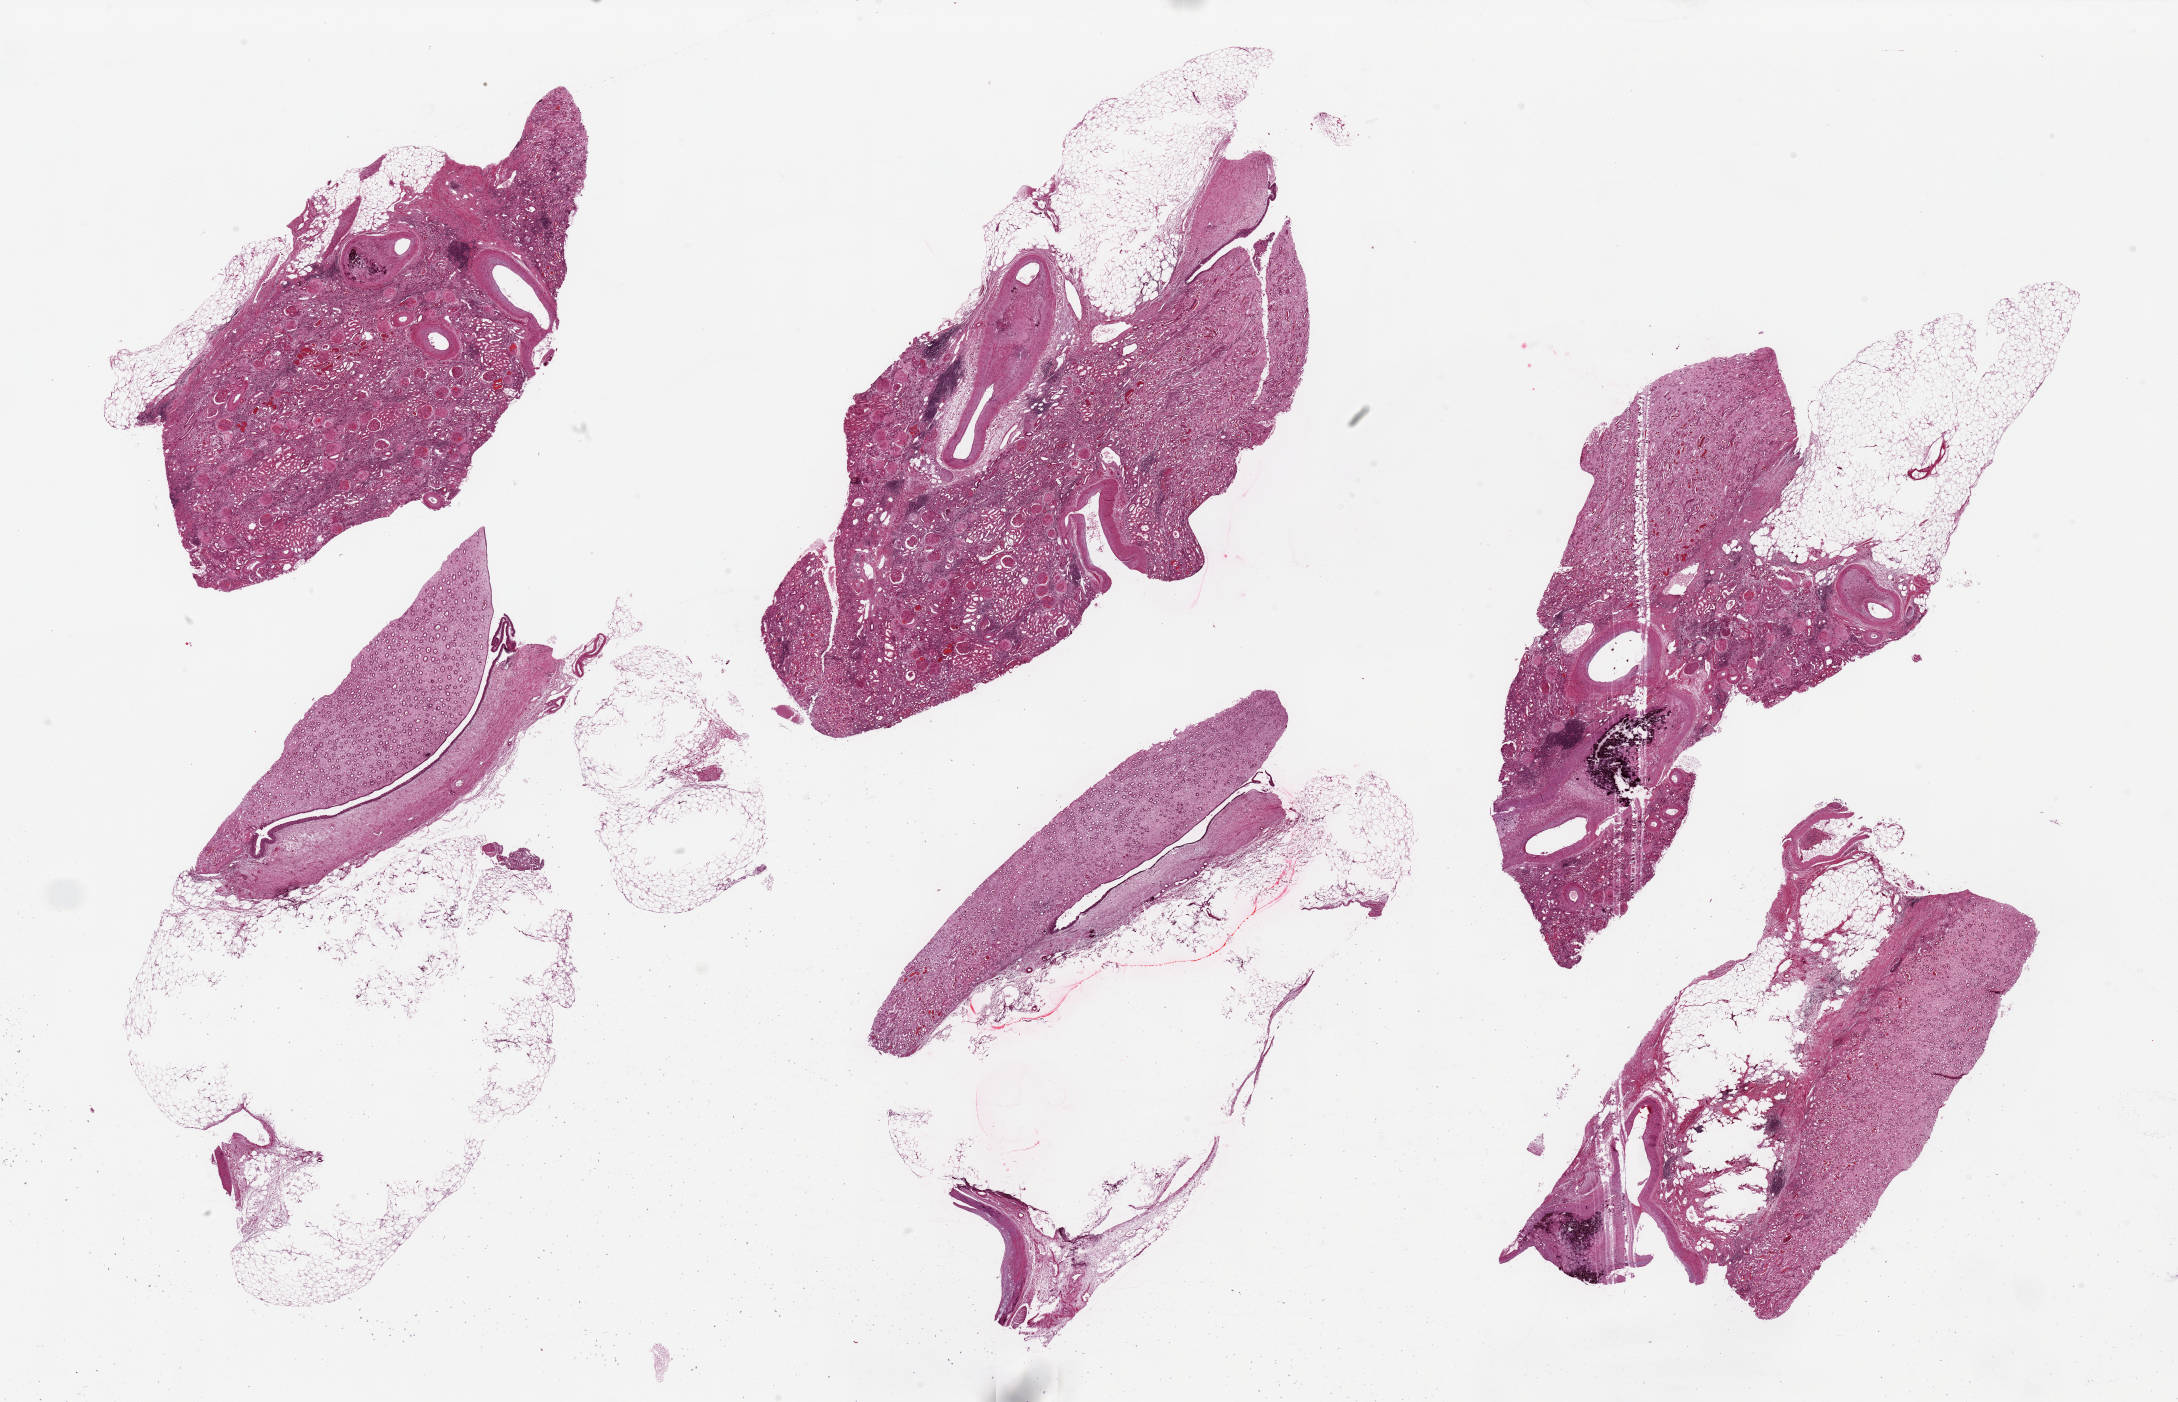
H&E whole-slide image, brightfield, whole scanned area (about 34.5 x 22.2 mm, acquisition: 20x scan) shown as a low-resolution overview; PAXgene-fixed, paraffin-embedded tissue; sampled site (target tissue): renal medulla; tissue donor sample. Donor sex: male.
• pathologist's review note for this sample: 6 pieces up to 10x6 mm; 3 are pure medulla, 3 are mixed medulla and cortex; cortex shows severe vascular lesions as in 0725; label medulla, consider it mixed